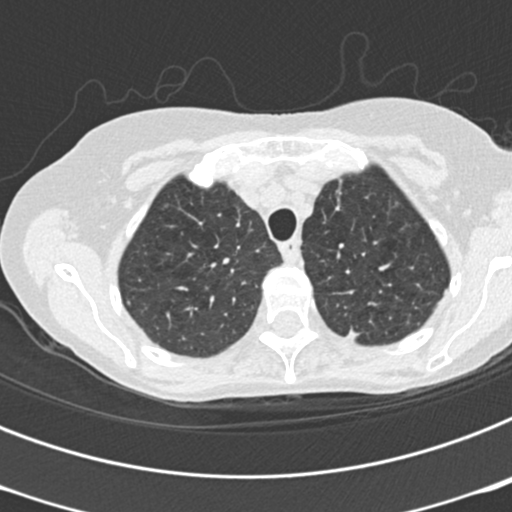
Low-dose screening chest CT, one axial slice; slice 167 of 199 in the series (ordered by position); reconstruction kernel B30f; 120 kVp; lung window (W 1500 / L -600 HU); 512 × 512 image matrix, field of view 290 × 290 mm.
Outlined on this slice (outlined manually by an expert reader):
- lesion 2 (nodule, upper lobe of left lung): bounding box <347,327,361,341> (left, top, right, bottom; pixels)